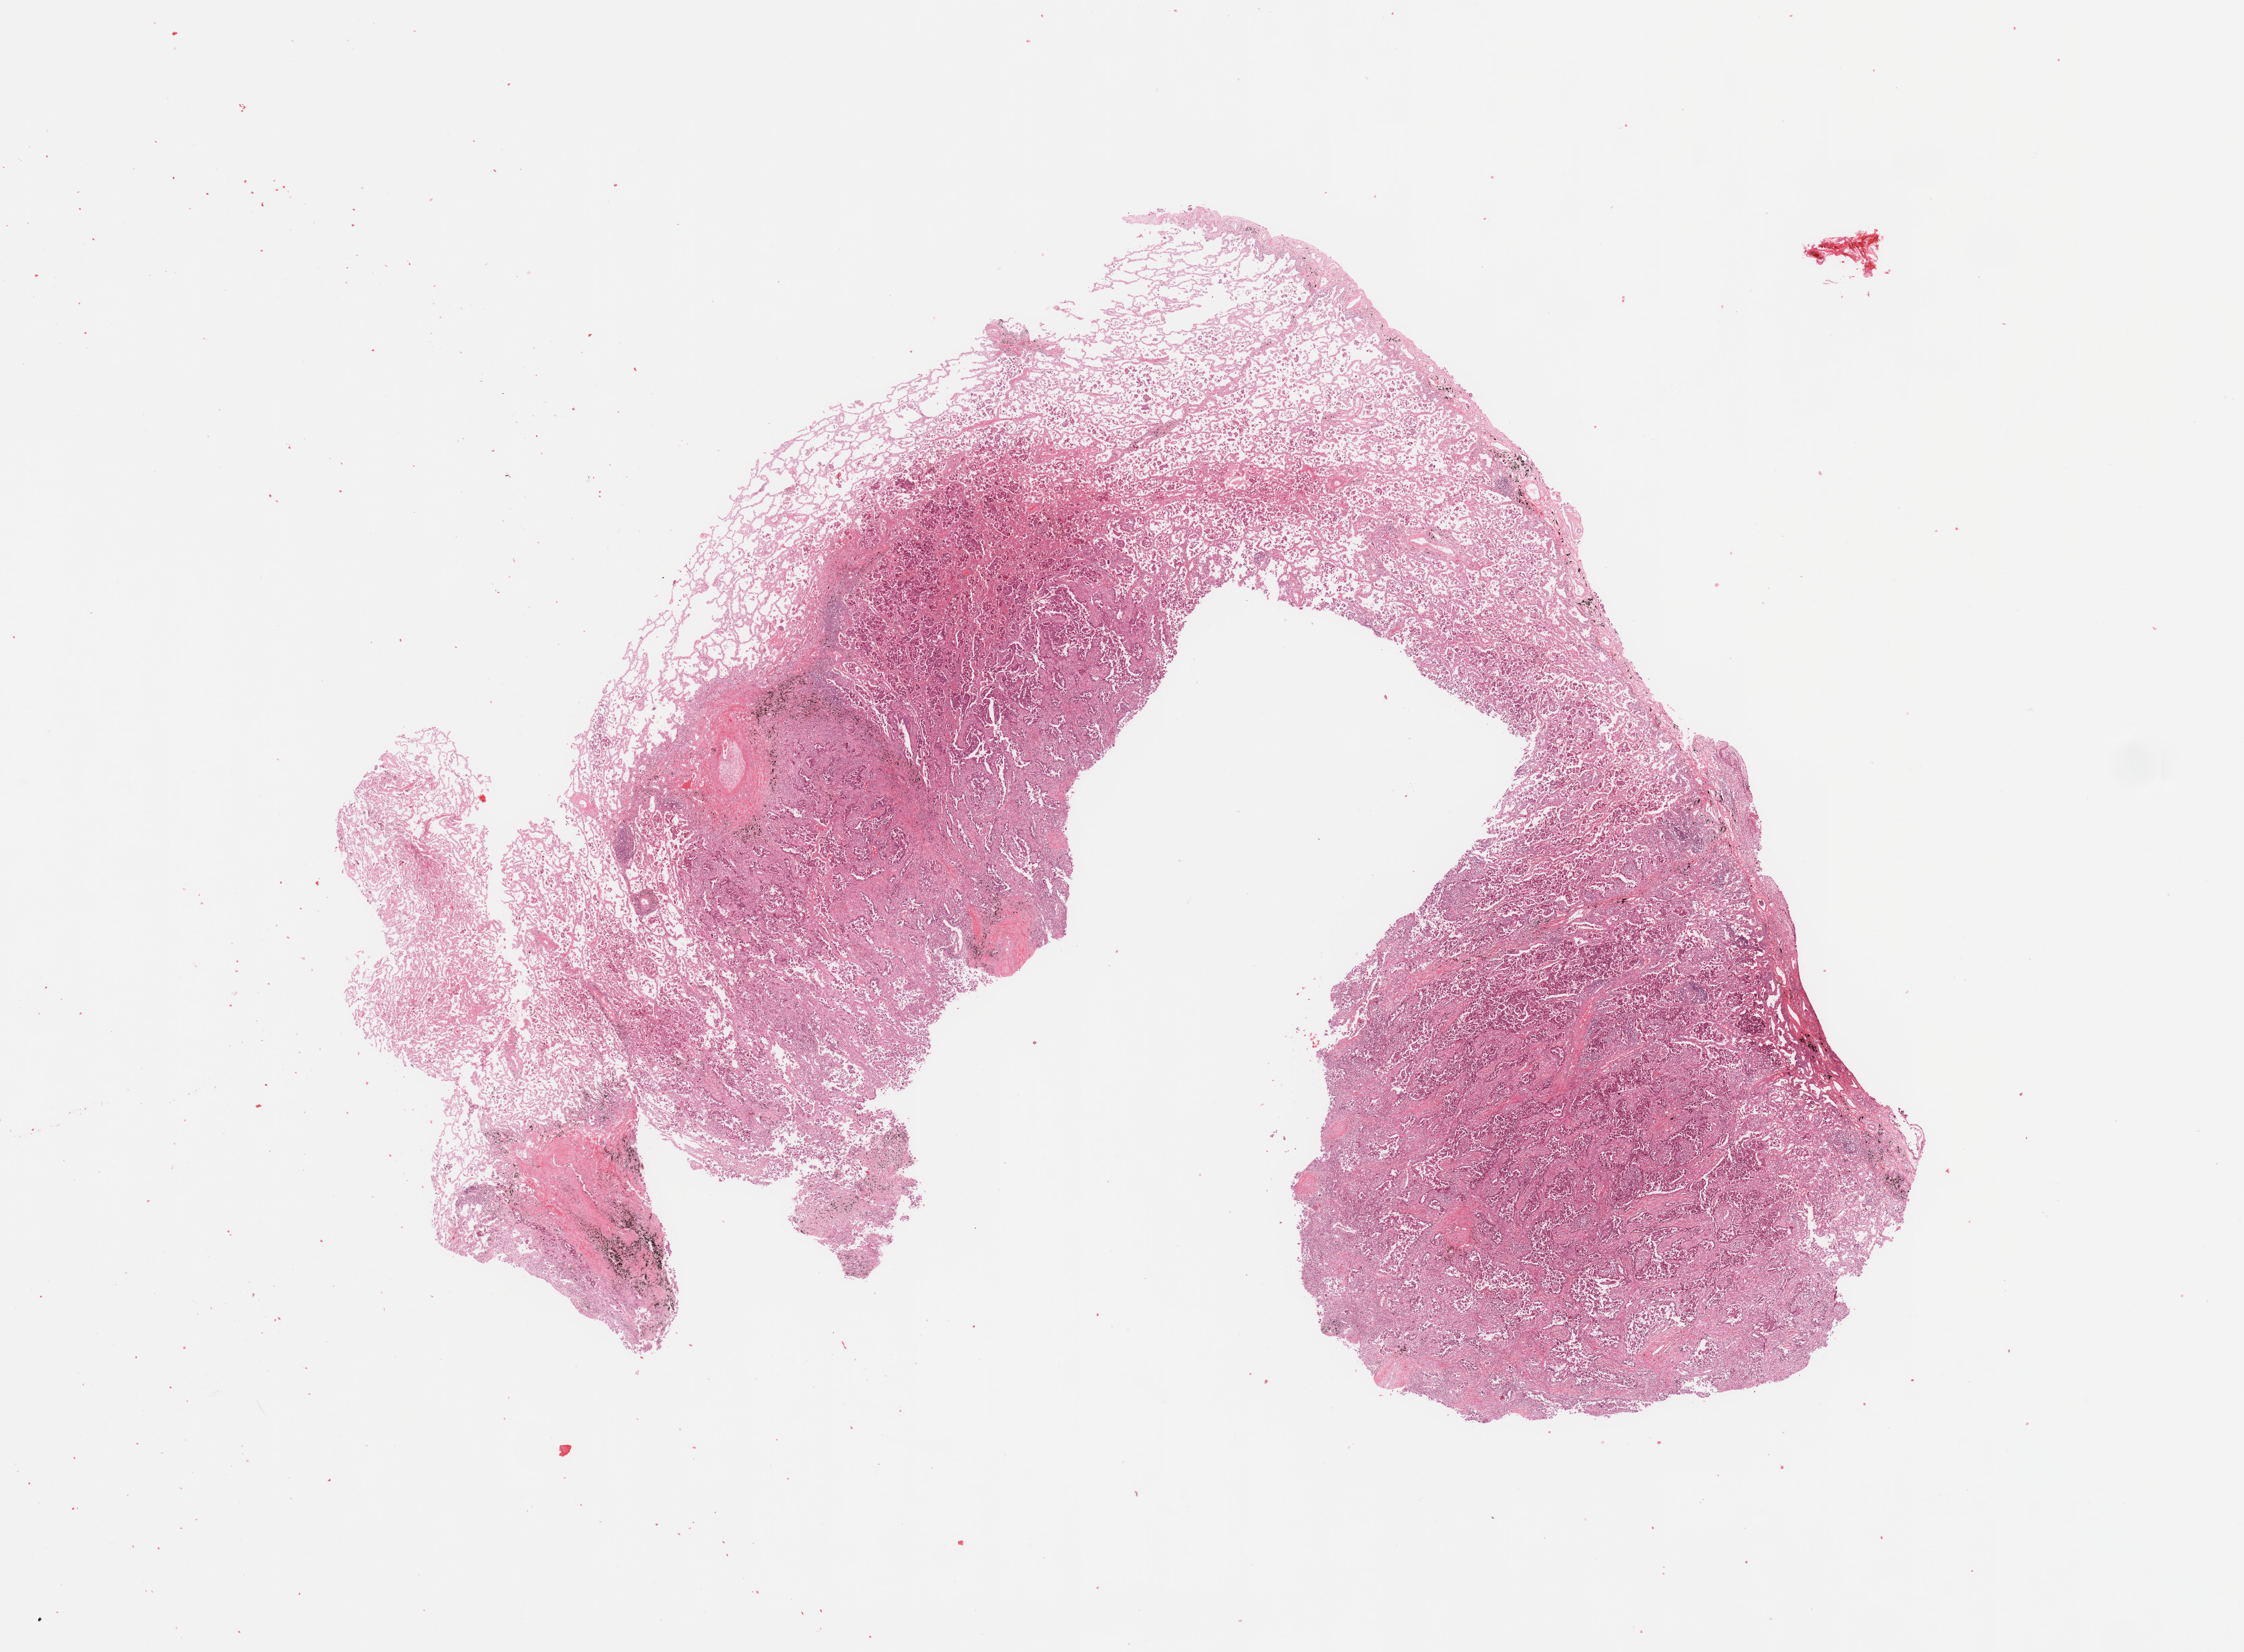
Digitized H&E tissue section (whole slide), whole scanned area (about 26.6 x 19.6 mm) shown as a low-resolution overview; lung, tumour tissue. 62-year-old male patient. Histologic grade: G3 (poorly differentiated).
Primary tumour site (as recorded): left upper lobe. Diagnosis: Adenocarcinoma, NOS. AJCC pathologic stage: IIIA.